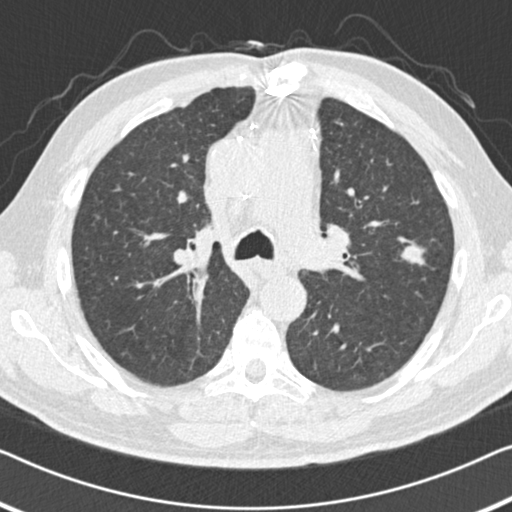
Low-dose screening chest CT, one axial slice. Position 102 of 155 along the scan axis. 120 kVp. Lung window (W 1500 / L -600 HU). 512 × 512 image matrix, field of view 332 × 332 mm.
Annotated regions visible in this slice (expert manual segmentation):
- lesion 1 (tumor, upper lobe of left lung): bounding box [x1, y1, x2, y2] px = [400, 243, 426, 266]